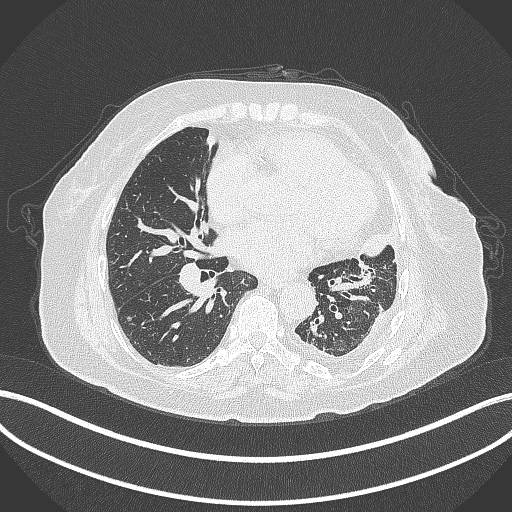
Chest CT, one axial slice; slice 164 of 399 in the series (ordered by position); 120 kVp; lung window (W 1500 / L -600 HU); 512 × 512 image matrix, field of view 400 × 400 mm. Female patient, age 75 years. Case-level facts recorded for this patient, not image findings: clinical TNM (as recorded): T3 N3 M1.
Annotated regions visible in this slice (bounding box drawn by a radiologist):
- lung tumour (recorded histology: adenocarcinoma): bounding box (x1, y1, x2, y2) in pixels: (358, 224, 397, 258)